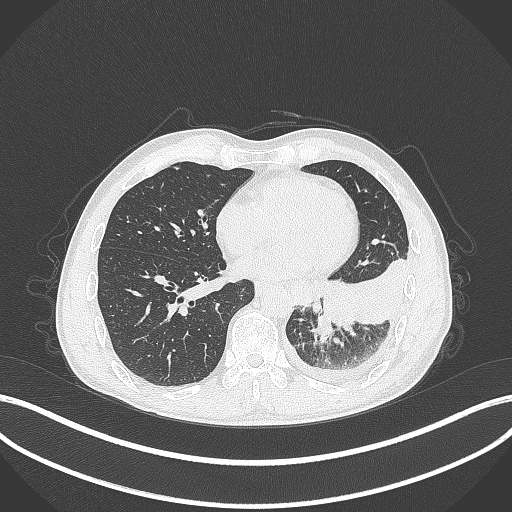
Chest CT, one axial slice; position 109 of 295 along the scan axis; reconstruction kernel B70f; lung window (W 1500 / L -600 HU); 1 mm slice thickness; 512 × 512 image matrix. Patient: male, 47 years. Case-level facts recorded for this patient, not image findings: clinical TNM (as recorded): T3 N1 M1c; histopathological grade: G3.
Outlined on this slice (rectangle marked by the reading radiologist):
- lung tumour (recorded histology: small cell carcinoma): box from (x=309, y=315) to (x=334, y=339) px